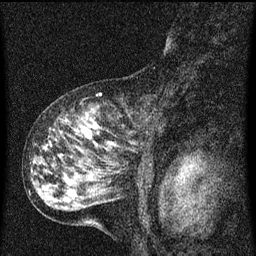
Breast MRI (dynamic contrast-enhanced), one sagittal slice. Dynamic contrast-enhanced series, image 2 of 3 at this slice position (ordered by acquisition). 1.5 T. TE 4.2 ms, TR 8 ms. 256 × 256 image matrix, field of view 180 × 180 mm. Female patient, age 55 years.
Annotated regions visible in this slice (semi-automatic segmentation, software-assisted and operator-edited):
- analysis volume of interest (the breast-tissue region the enhancement analysis was run in; not a lesion): bounding box <38,92,157,159> (left, top, right, bottom; pixels)
- tumour enhancement mask (voxels above the 70 % enhancement threshold inside the analysis volume of interest): <78,114,115,147>